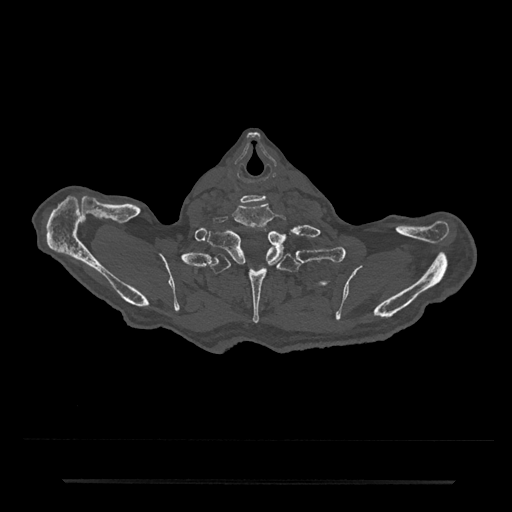
CT including the spine, one axial slice. Slice 713 of 797 in the series (ordered by position). 120 kVp. Bone window (W 1800 / L 400 HU). 0.5 mm slice thickness. 512 × 512 image matrix, field of view 427 × 427 mm. Male patient, age 74 years. From the clinical record (not read from this slice): primary cancer: prostate.
Structures marked on this image (semi-automatic segmentation, software-assisted and operator-edited):
- T1 vertebra: bounding box [x1, y1, x2, y2] px = [208, 227, 285, 267]
- T2 vertebra: [210, 248, 306, 323]